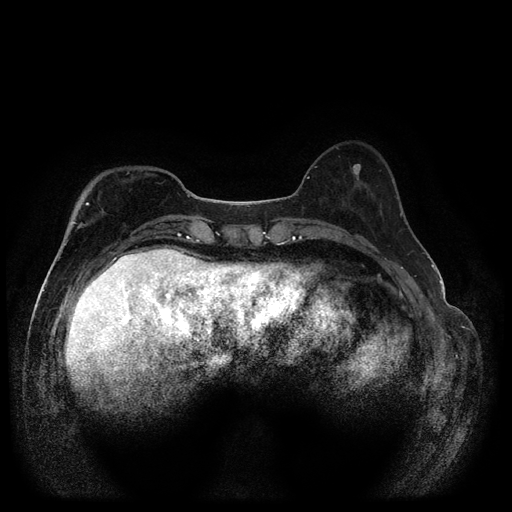
Breast MRI (dynamic contrast-enhanced, multi-phase), one axial slice. Slice 33 of 116 in the series (ordered by position). Dynamic contrast-enhanced series, time point 2 of 5 at this slice position (early post-contrast). 1.5 T. TE 2.6 ms, TR 5.4 ms. 2 mm slice thickness. 512 × 512 image matrix, field of view 340 × 340 mm. Female patient, age 51 years.
Annotated regions visible in this slice (semi-automatic segmentation, software-assisted and operator-edited):
- breast lesion (labelled benign in the annotation): bounding box [x1, y1, x2, y2] px = [352, 163, 363, 181]